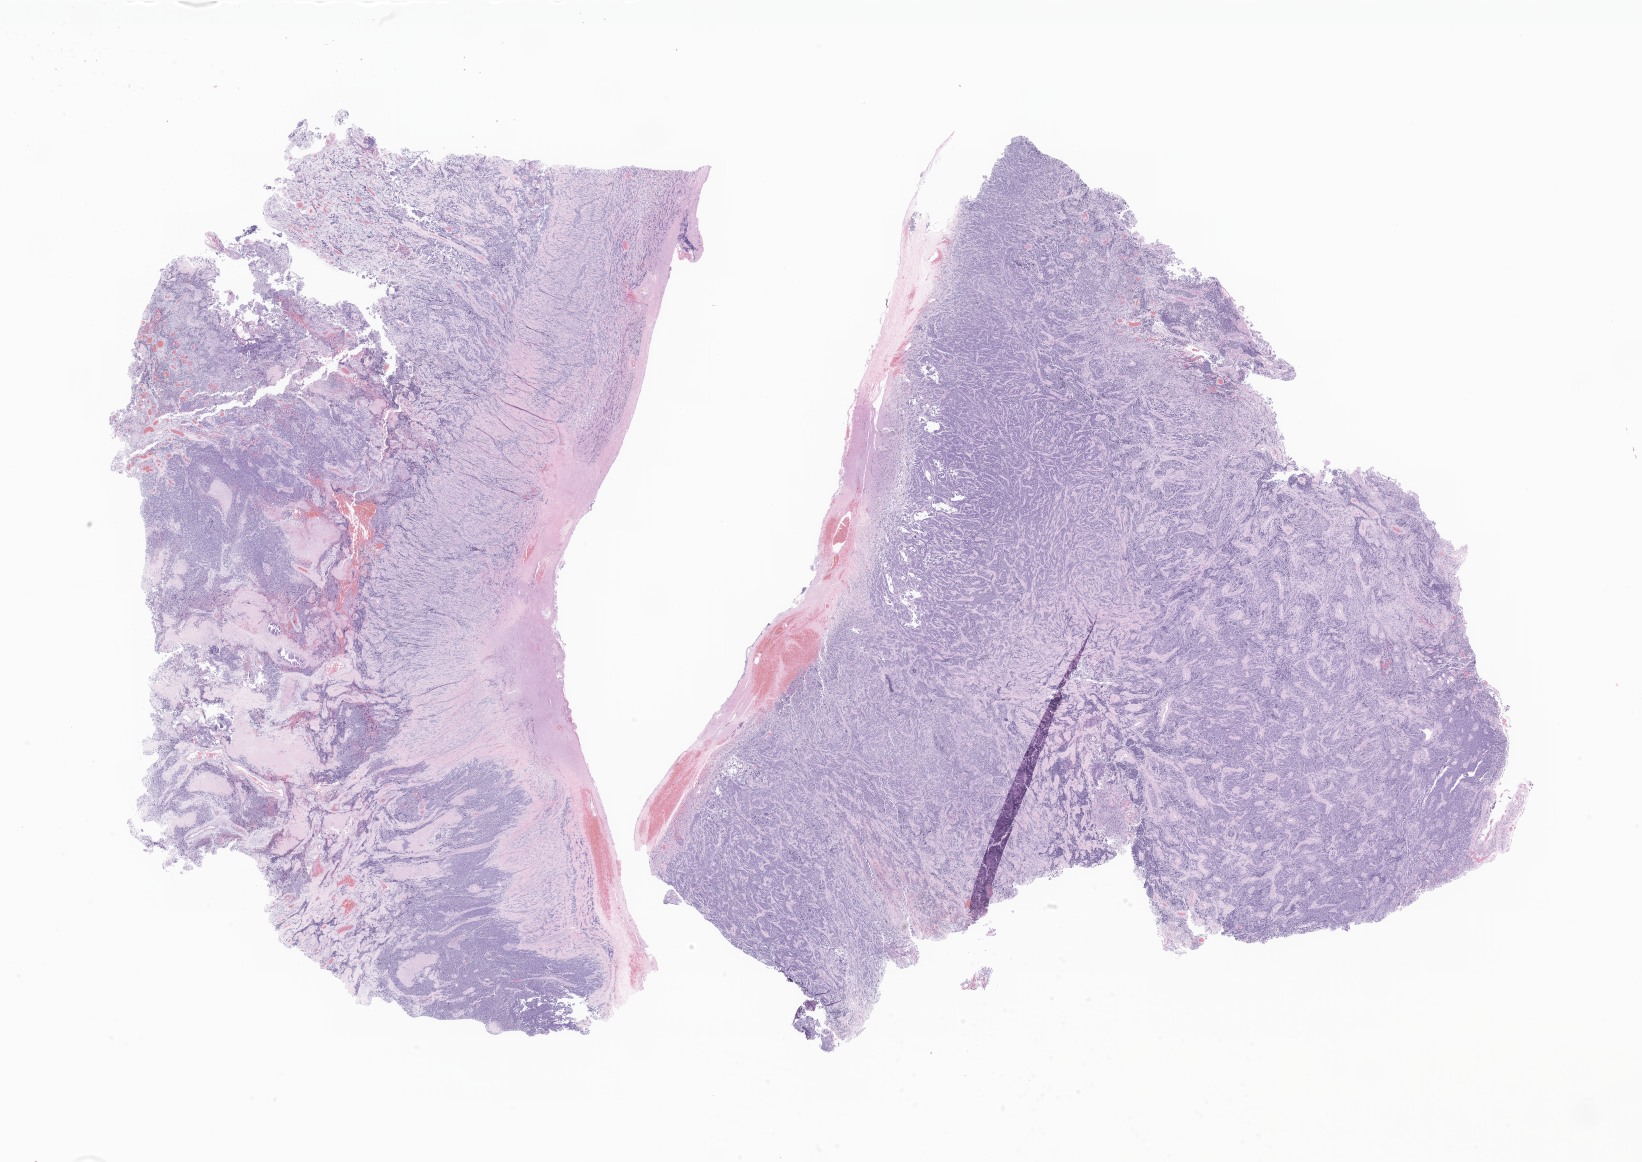
Digitized haematoxylin and eosin-stained section of tumor tissue from the frontal lobe, low-resolution overview of the scanned area, about 27.7 x 19.6 mm; FFPE section. Patient female; age 823 days (about 2.3 years).
Diagnosis (ICD-O-3 morphology term): Neoplasm, malignant.